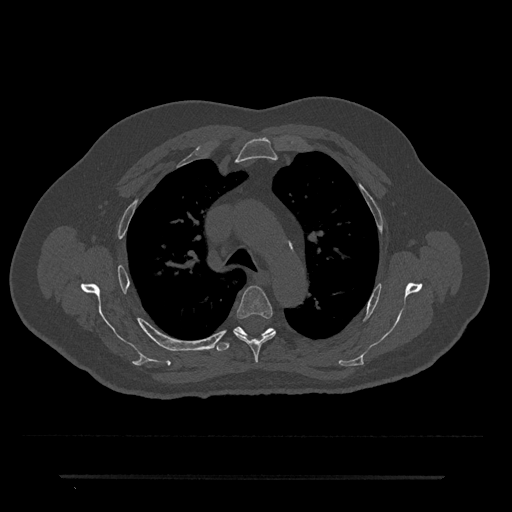
CT including the spine, one axial slice; position 515 of 797 along the scan axis; reconstruction kernel Br40s/3; bone window (W 1800 / L 400 HU); 0.5 mm slice thickness; 512 × 512 image matrix, field of view 437 × 437 mm. Male patient, age 69 years. From the clinical record (not read from this slice): primary cancer: prostate.
Structures marked on this image (semi-automatic segmentation, software-assisted and operator-edited):
- T4 vertebra: box from (x=234, y=286) to (x=276, y=363) px
- T5 vertebra: (x=214, y=327)–(x=275, y=351)